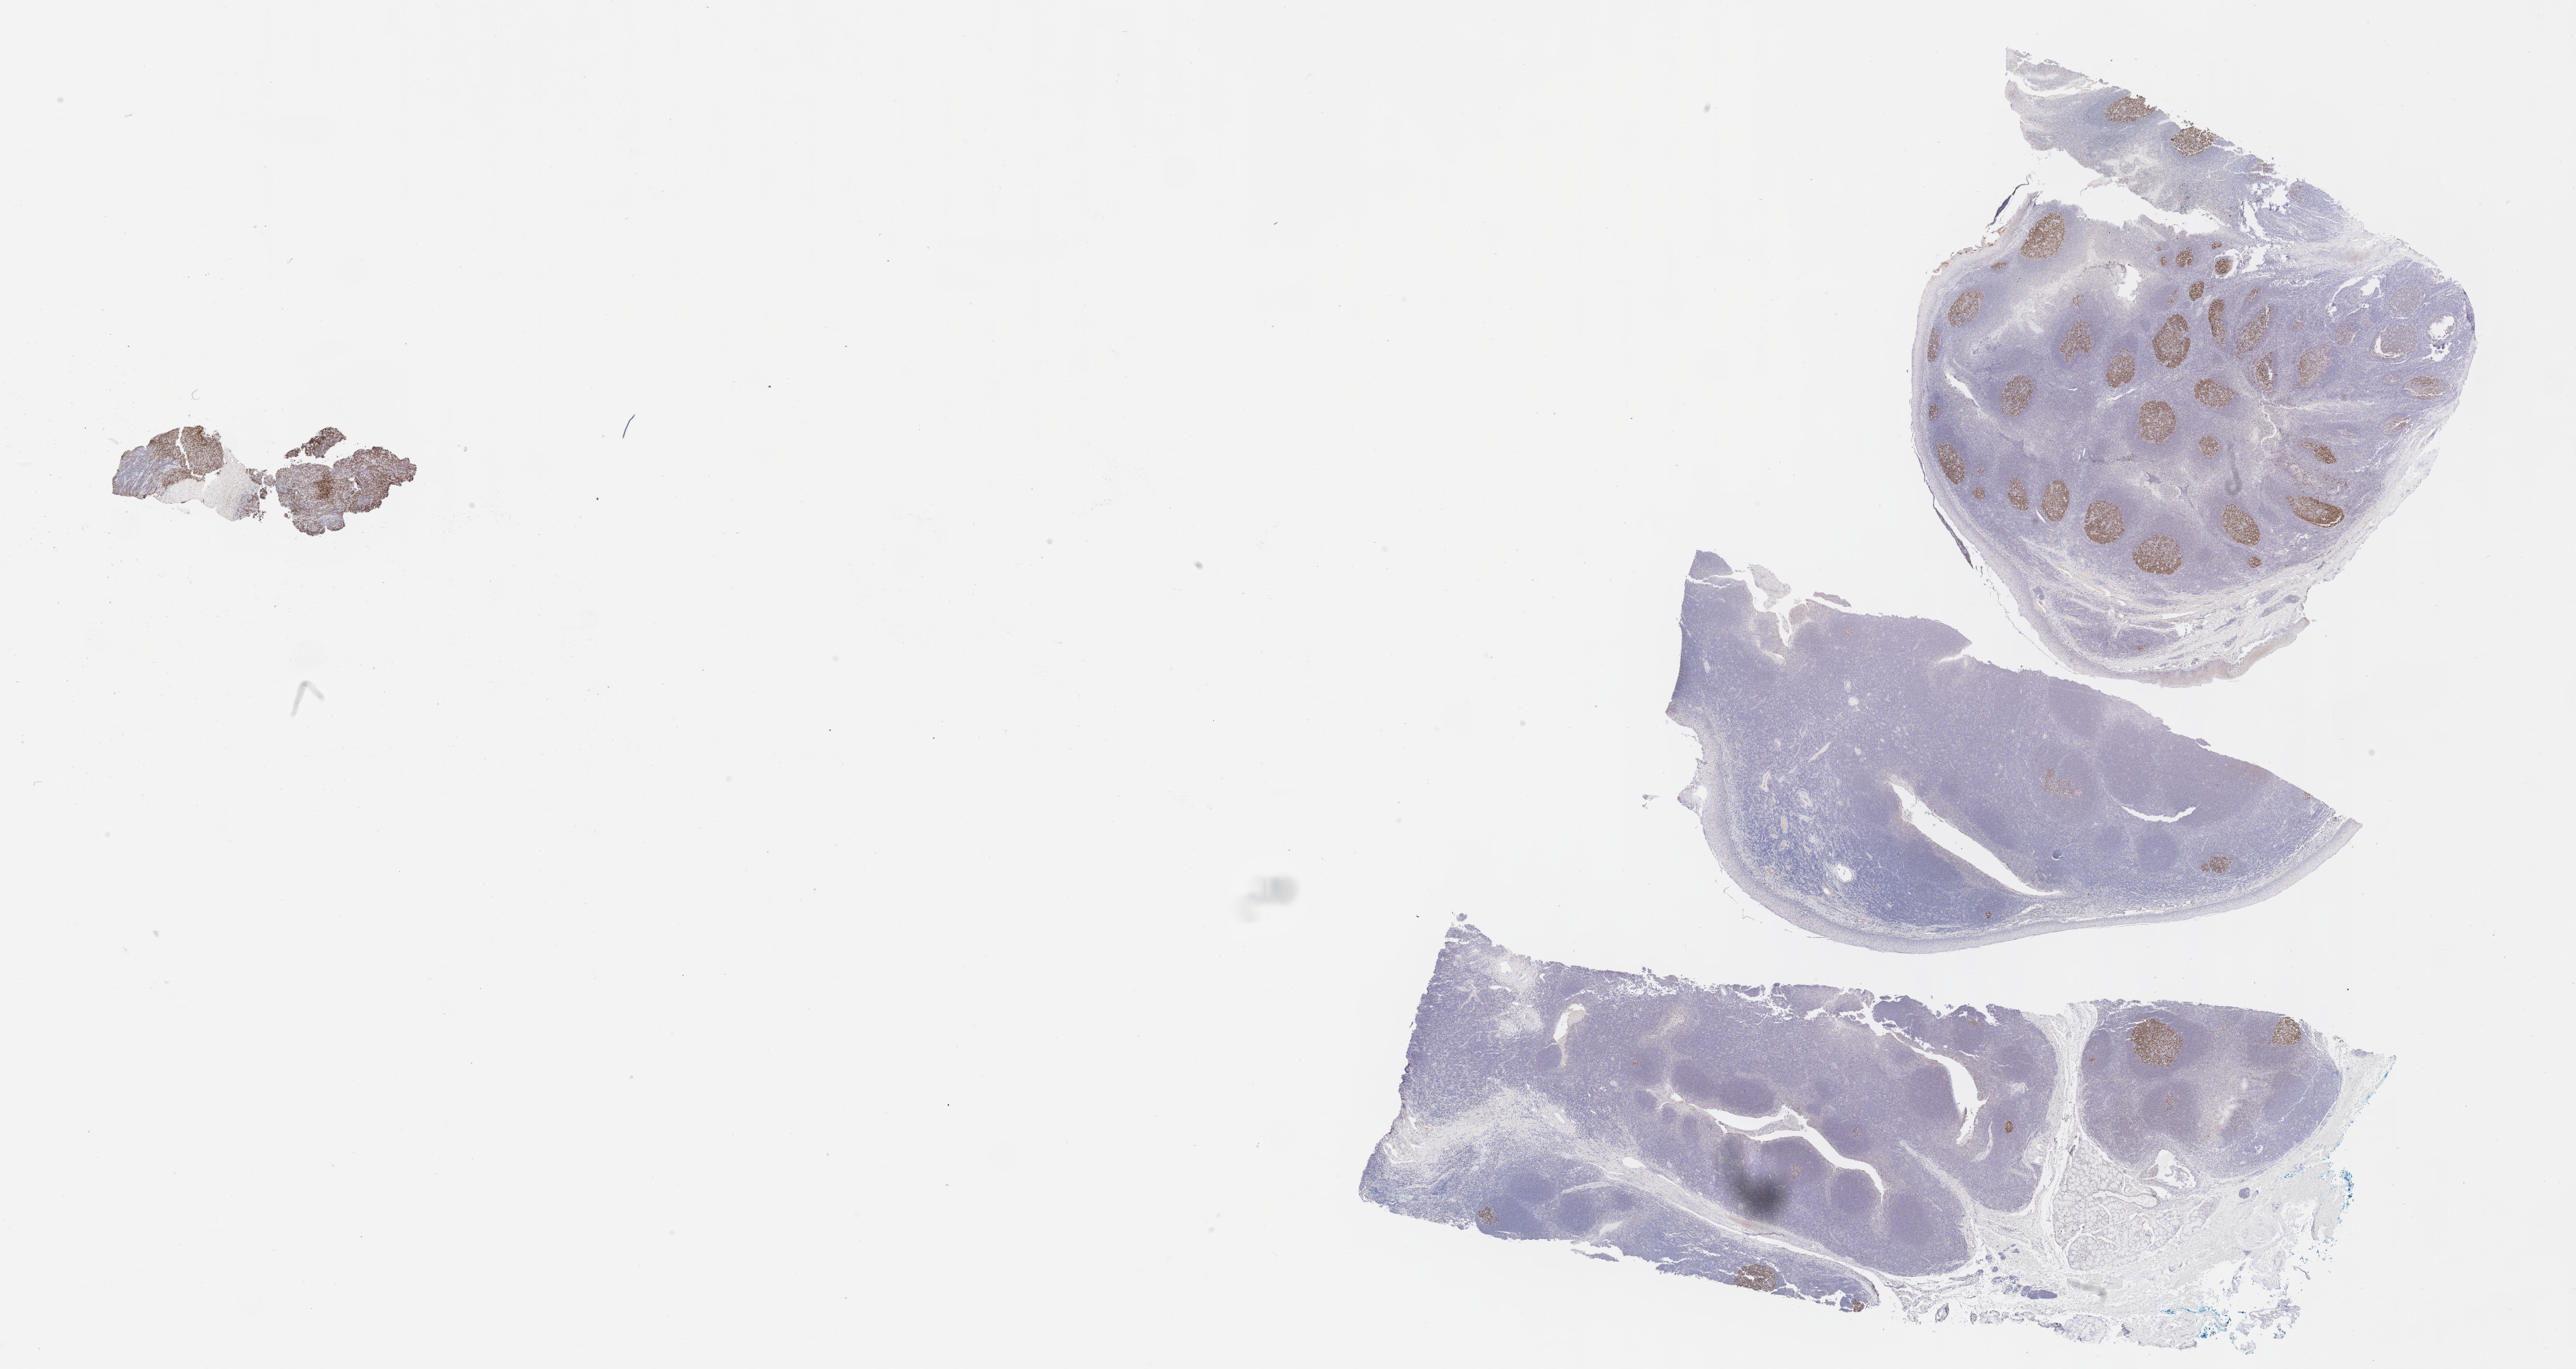
Immunohistochemistry (IHC) whole-slide image stained for BCL6, shown as a low-resolution overview of the whole scanned area (about 28.7 x 15.2 mm), specimen: tumor tissue. Patient male; age 15 years.
Histologic diagnosis: Burkitt lymphoma, NOS.